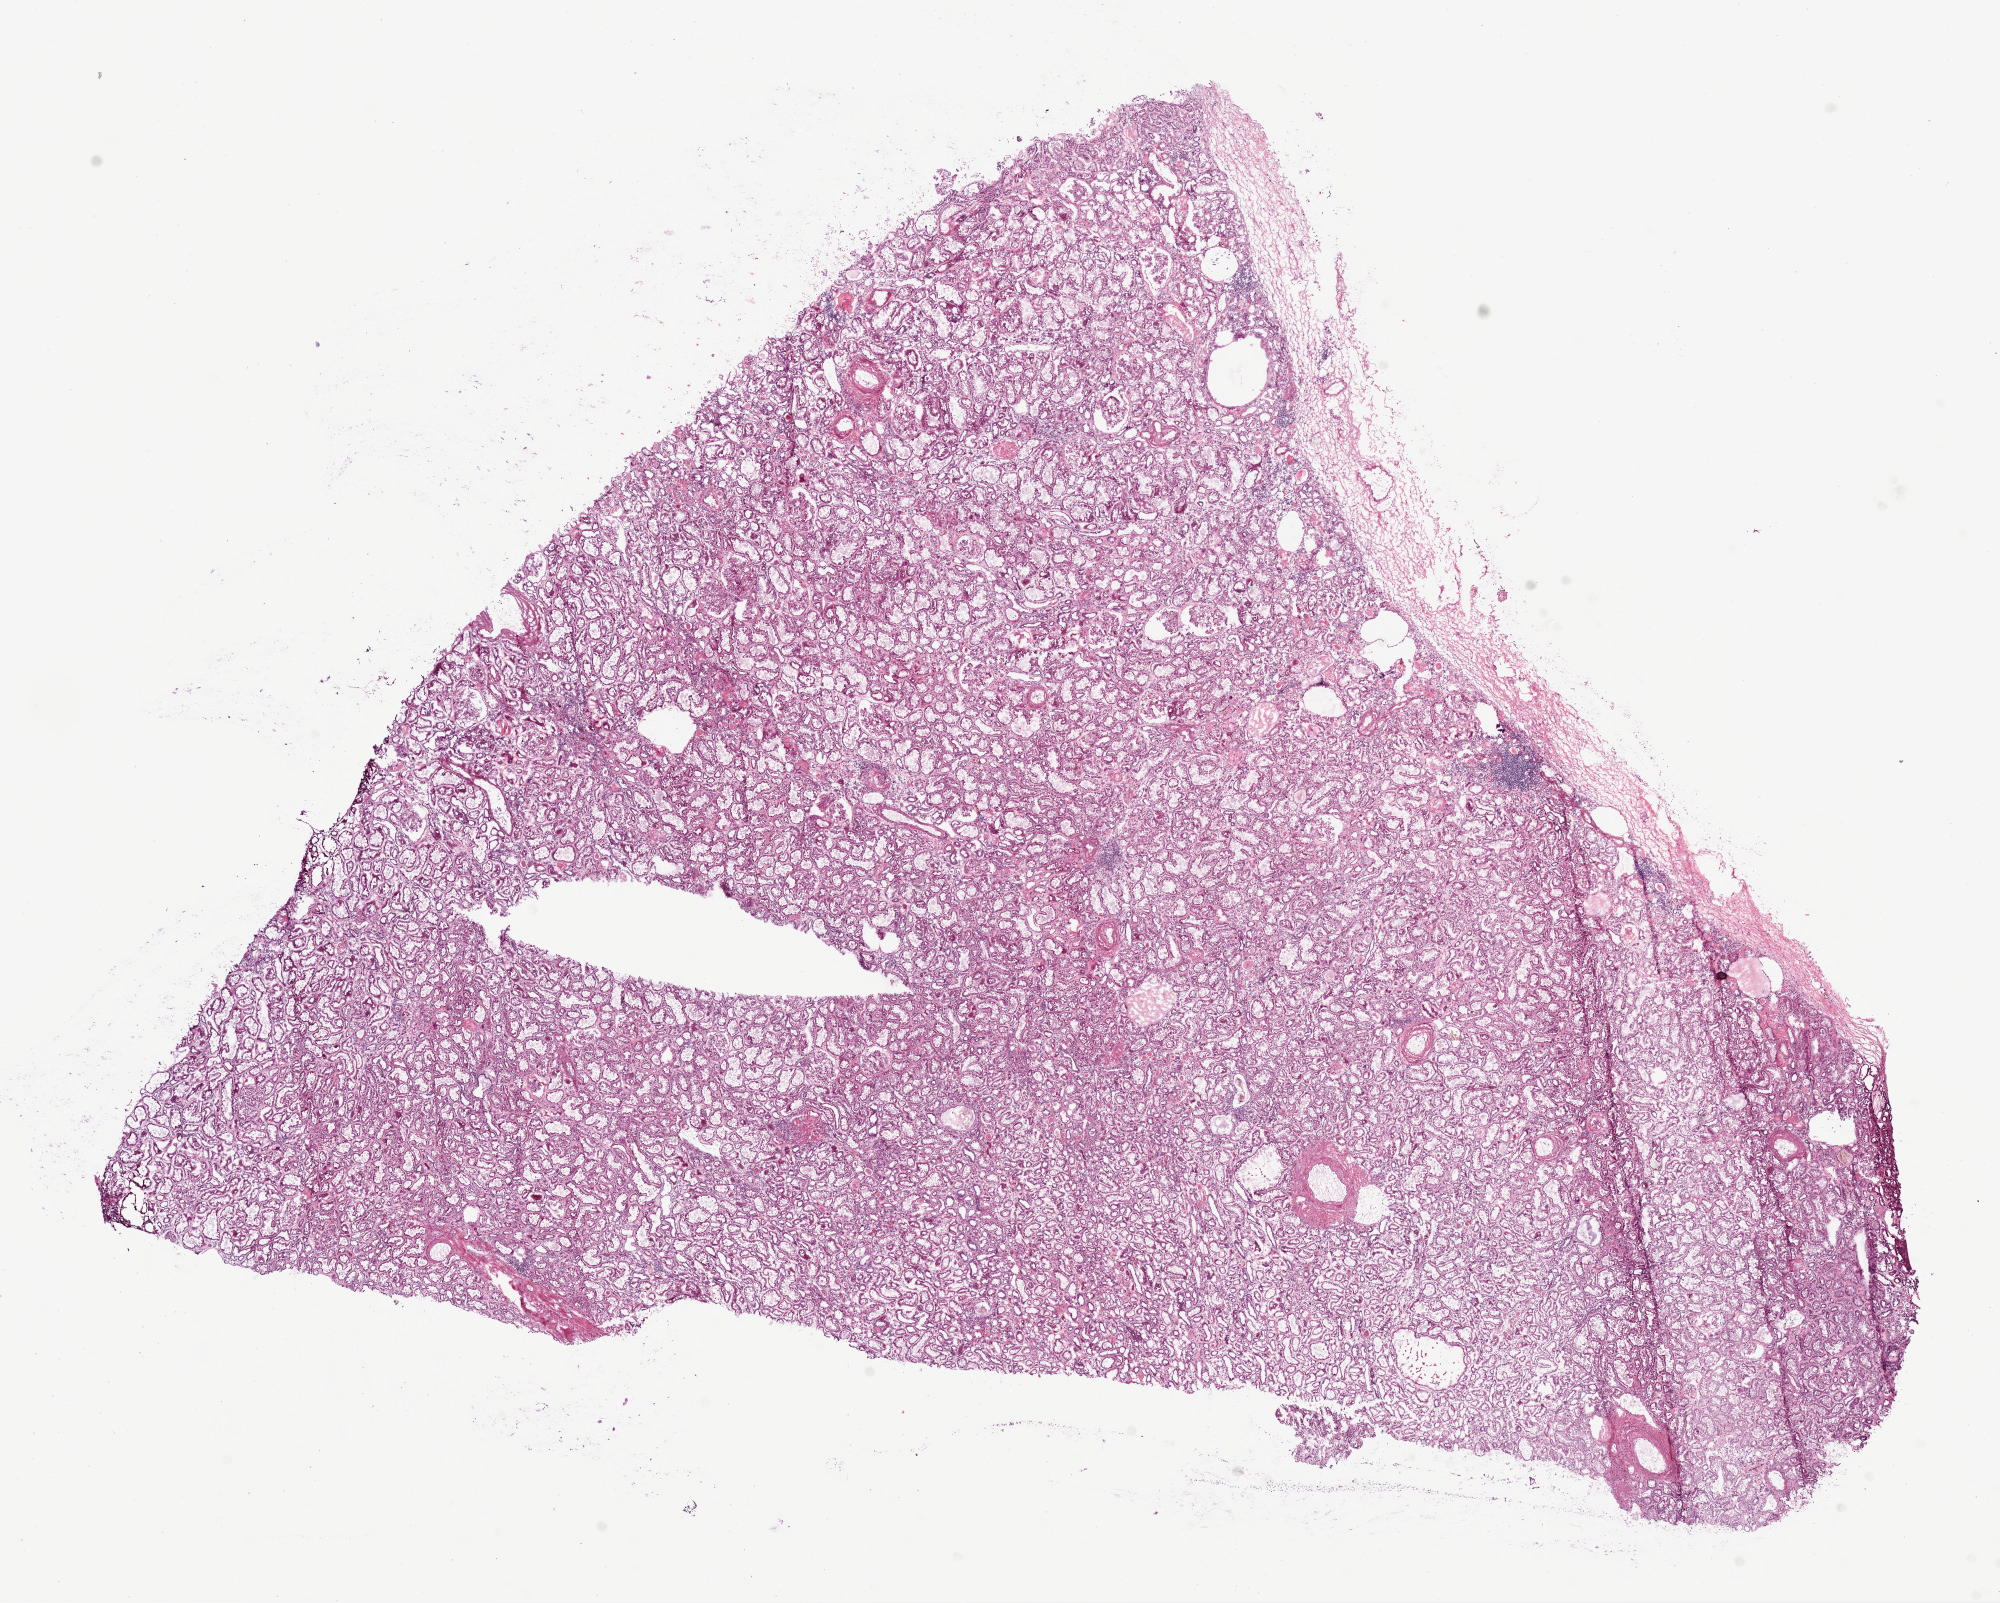
H&E whole-slide image — whole scanned area (about 16.0 x 12.9 mm, from a 20x scan) shown as a low-resolution overview. Frozen section from the bottom of the tissue portion. Solid tissue normal (non-tumour tissue) sample from the kidney. Patient: female, age at initial diagnosis 80 years.
- this section: solid tissue normal (non-tumour) sample from the same patient
- patient diagnosis: Clear cell adenocarcinoma, NOS